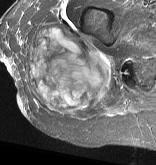
MRI of an extremity soft-tissue mass, one axial slice; slice 22 of 57 in the series (ordered by position); STIR; MR volume resampled by the dataset authors to the PET/CT grid (not the native acquisition matrix); 156 × 165 image matrix, field of view 152 × 161 mm. Female patient. From the clinical record (not read from this slice): histological type: epithelioid sarcoma with vascular differentiation; site of the primary tumour: right buttock.
Annotated regions visible in this slice (expert contour drawn on MRI and transferred to this co-registered scan by the dataset authors):
- gross tumour volume (mass): bounding box (x1, y1, x2, y2) in pixels: (26, 23, 112, 115)